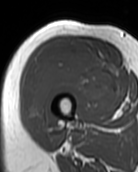
MRI of an extremity soft-tissue mass, one axial slice; slice 38 of 99 in the series (ordered by position); MR volume resampled by the dataset authors to the PET/CT grid (not the native acquisition matrix); 3.27 mm slice thickness; 138 × 172 image matrix, field of view 135 × 168 mm. Female patient. From the clinical record (not read from this slice): histological type: pleiomorphic undifferentiated sarcoma; grade: high; site of the primary tumour: right quadricep.
Structures marked on this image (expert contour drawn on MRI and transferred to this co-registered scan by the dataset authors):
- gross tumour volume including surrounding oedema: bounding box <25,41,111,128> (left, top, right, bottom; pixels)
- gross tumour volume (mass): <25,41,111,128>